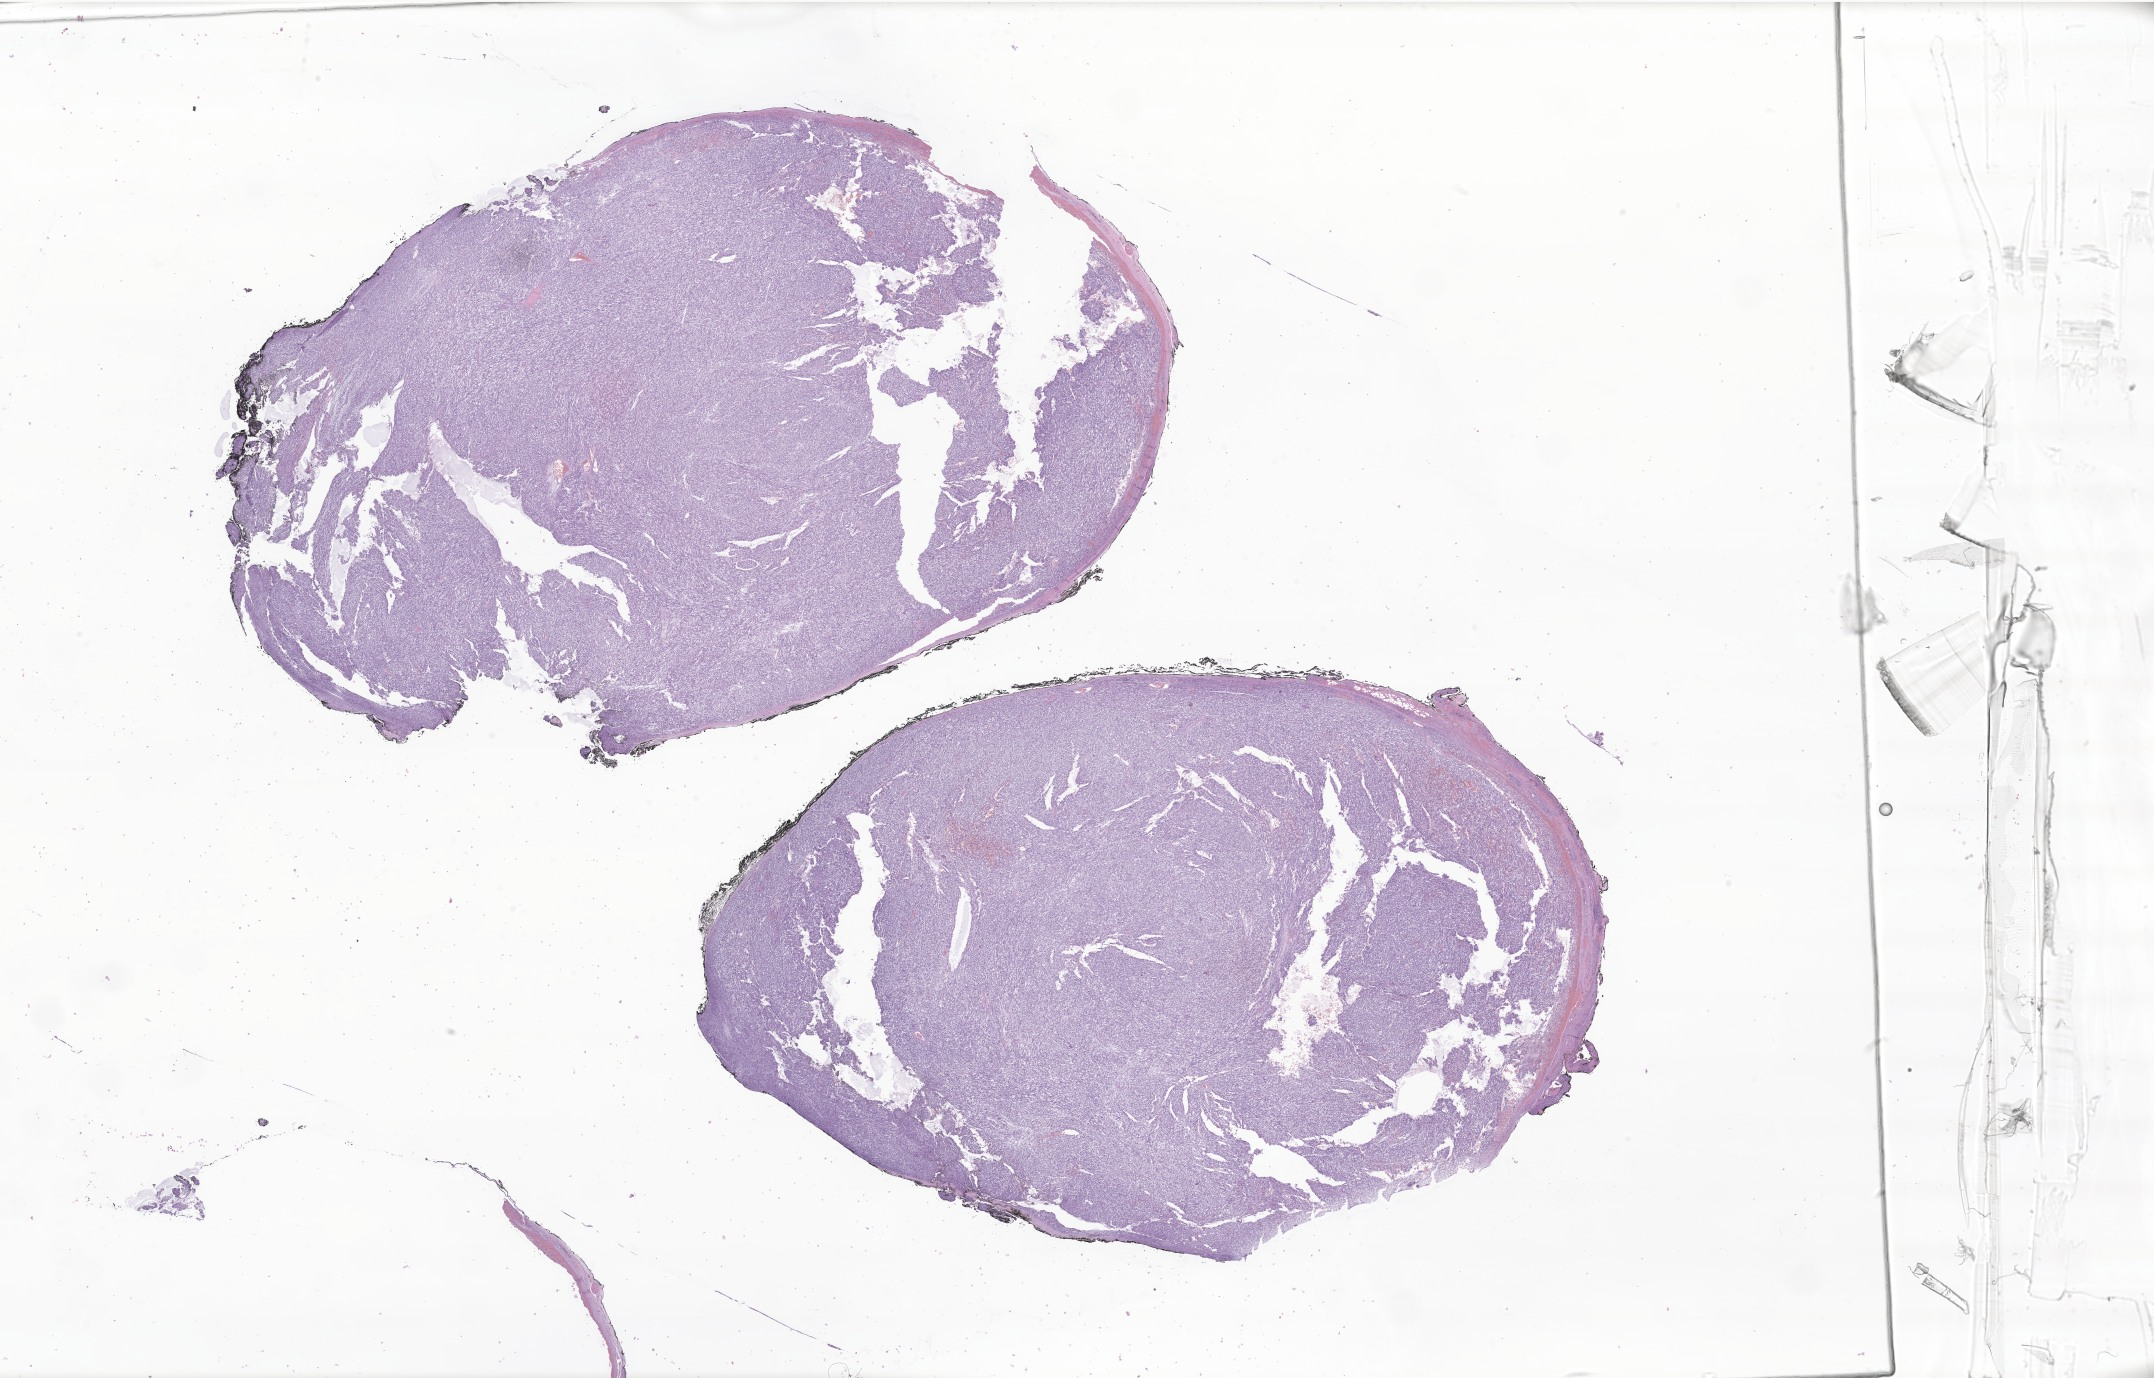
Hematoxylin and eosin (H&E) whole-slide image of tumor tissue from the eye, a low-resolution overview of the entire scanned area, about 36.3 x 23.2 mm; formalin-fixed paraffin-embedded section. Patient male; age 205 months (17 years 1 month).
Diagnosis: Rhabdomyoma, NOS.